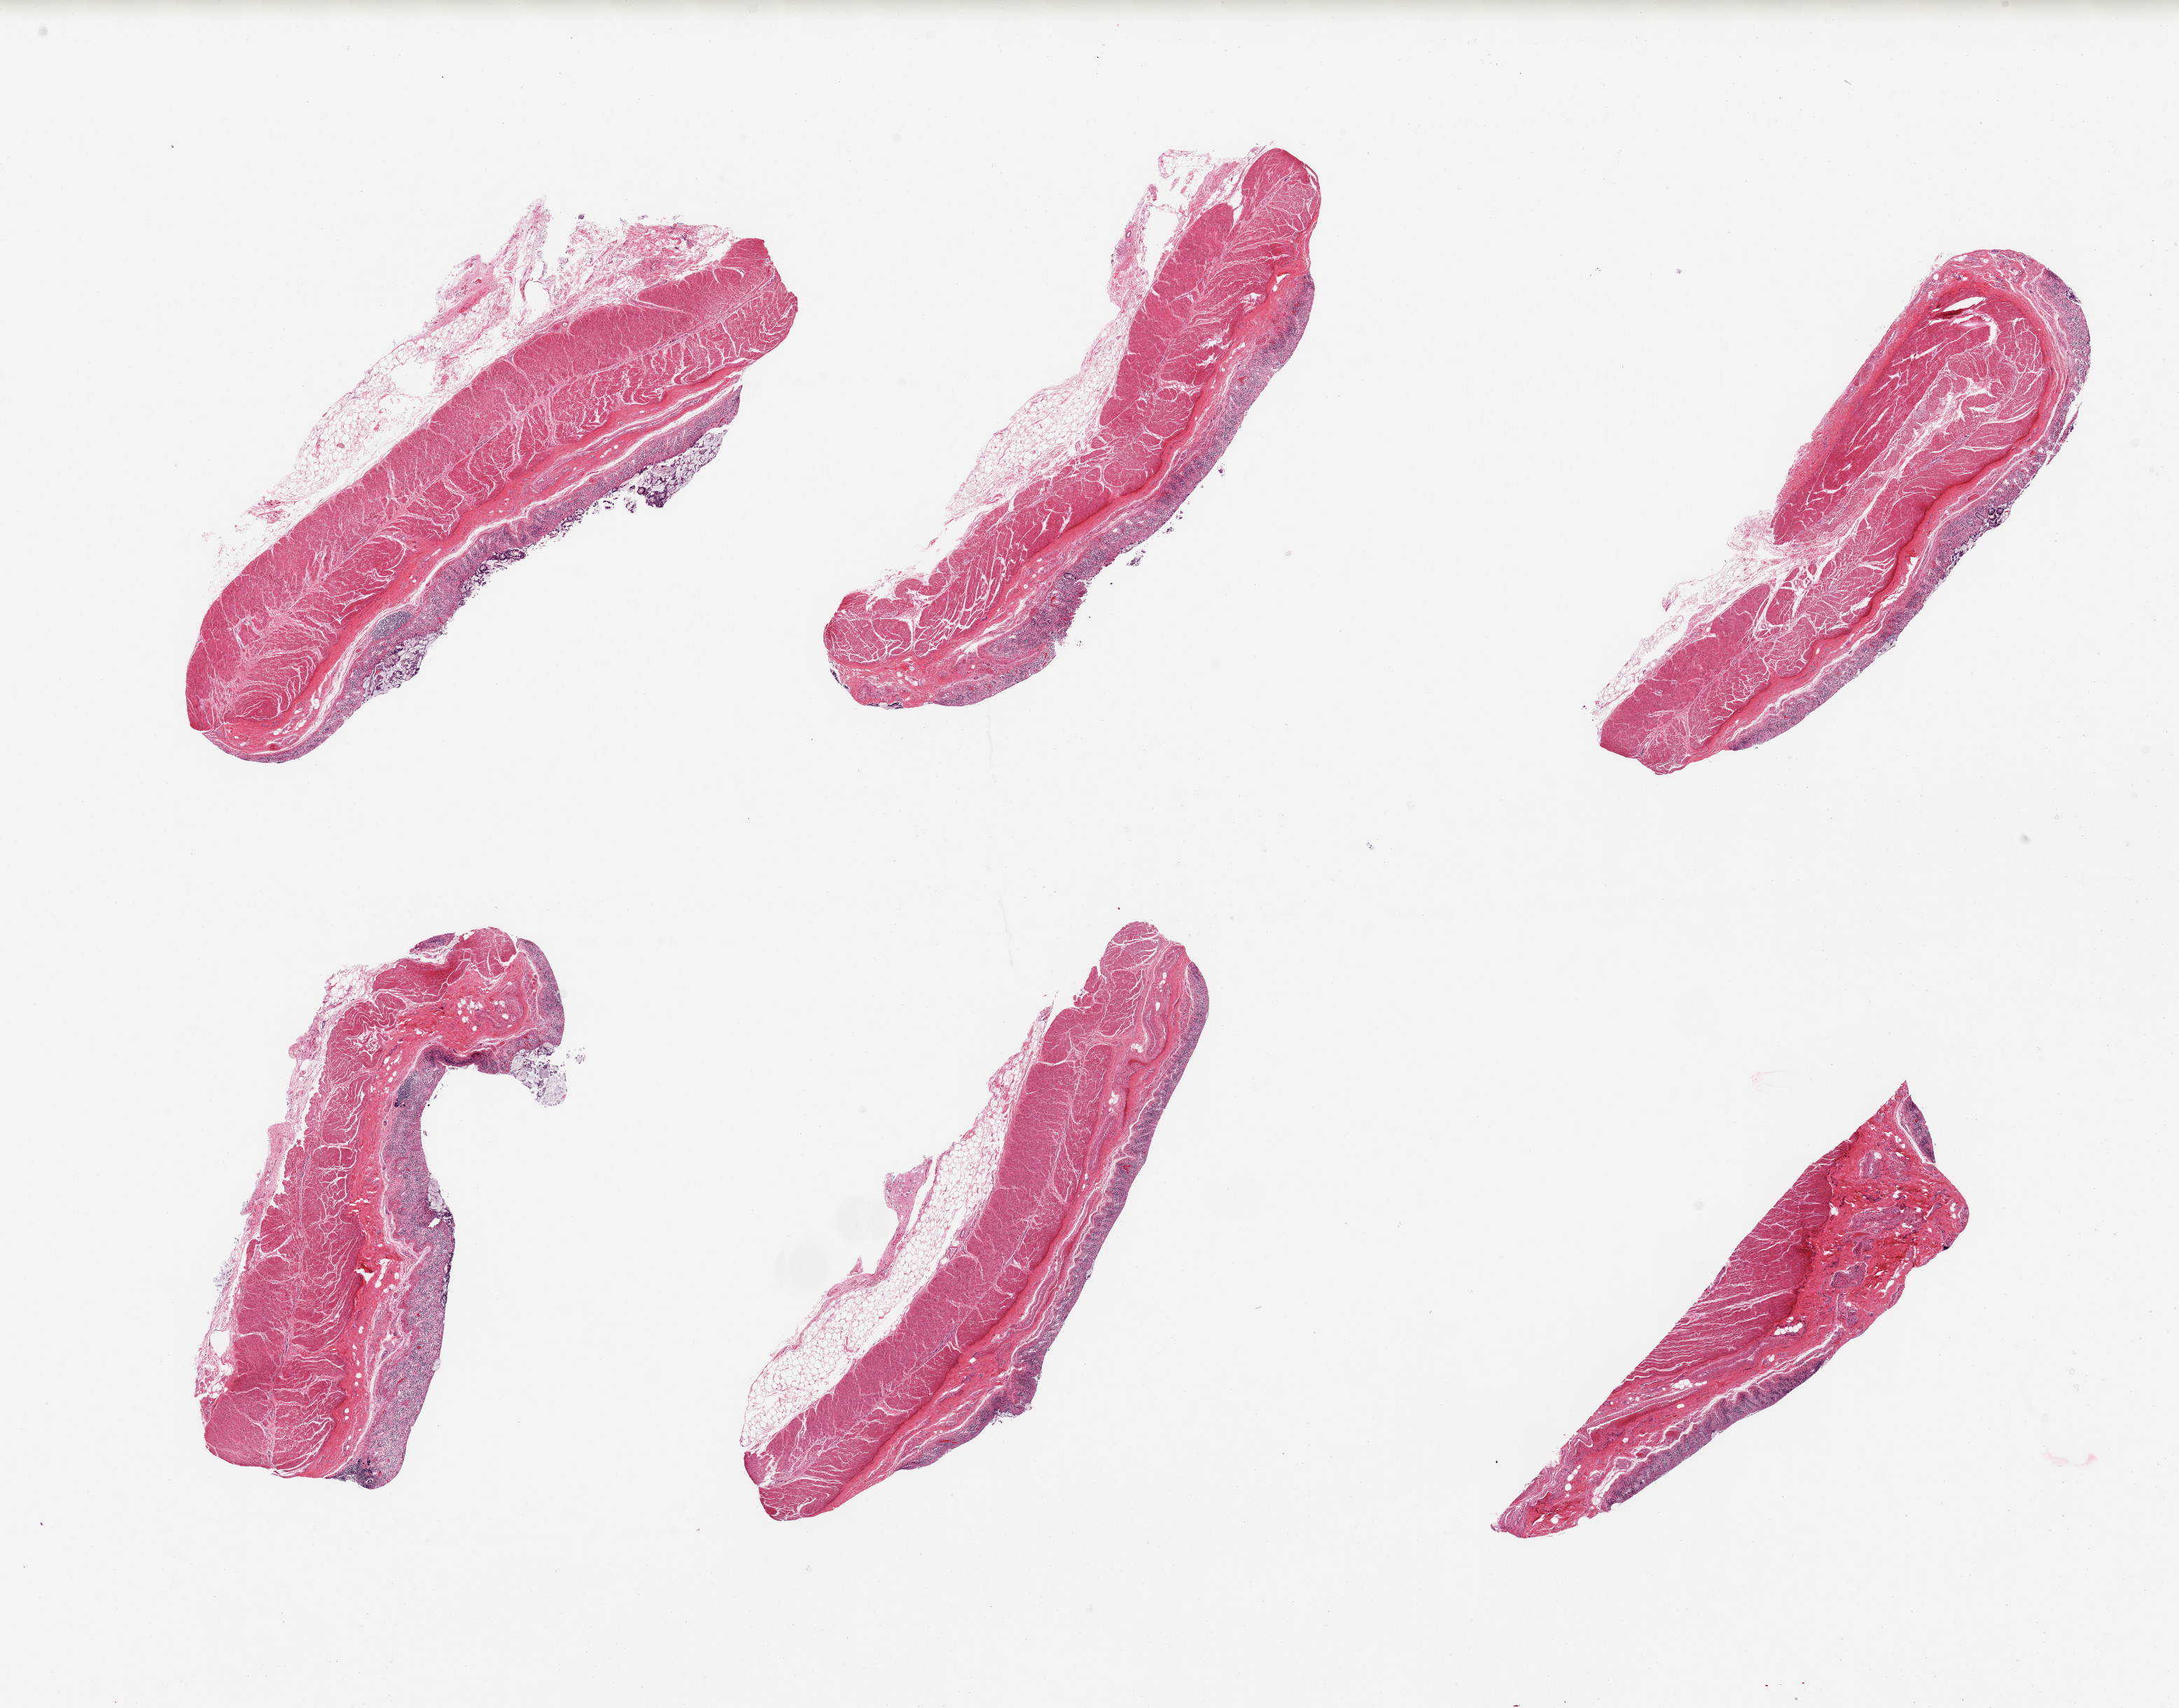
Digitized haematoxylin and eosin-stained section, shown as a low-resolution overview of the whole scanned area (about 24.6 x 19.3 mm, acquisition: 20x scan); PAXgene-fixed paraffin-embedded (PFPE) section; target tissue: transverse colon; tissue donor sample. Female donor.
Review note (as recorded): 6 pieces, mucosa badly autolyzed/sloughing.